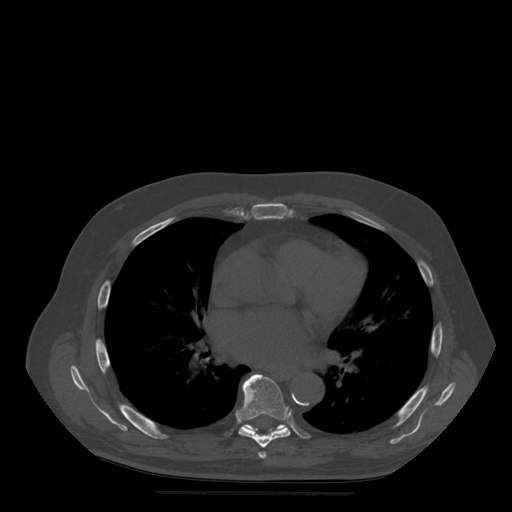
CT including the spine, one axial slice. Position 329 of 522 along the scan axis. Bone window (W 1800 / L 400 HU). 512 × 512 image matrix. Patient age 72 years. From the clinical record (not read from this slice): primary cancer: prostate.
Annotated regions visible in this slice (semi-automatic segmentation, software-assisted and operator-edited):
- T6 vertebra: bounding box (x1, y1, x2, y2) in pixels: (259, 452, 267, 459)
- T7 vertebra: (237, 374, 291, 448)
- T8 vertebra: (245, 425, 287, 432)